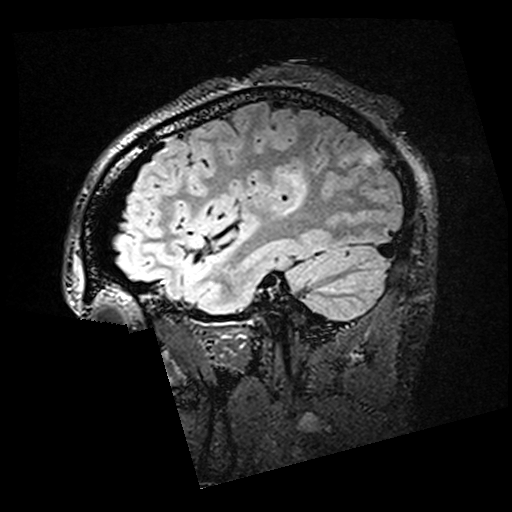
Brain MRI from a brain-tumour surgery series, one sagittal slice. Slice 47 of 176 in the series (ordered by position). T2 FLAIR. 1 mm slice thickness. 512 × 512 image matrix, field of view 250 × 250 mm. From the clinical record (not read from this slice): histopathology: Oligodendroglioma; WHO grade: 2; IDH mutation: yes.
Annotated regions visible in this slice (outlined manually by an expert reader):
- residual tumour: bounding box <282,172,306,192> (left, top, right, bottom; pixels)